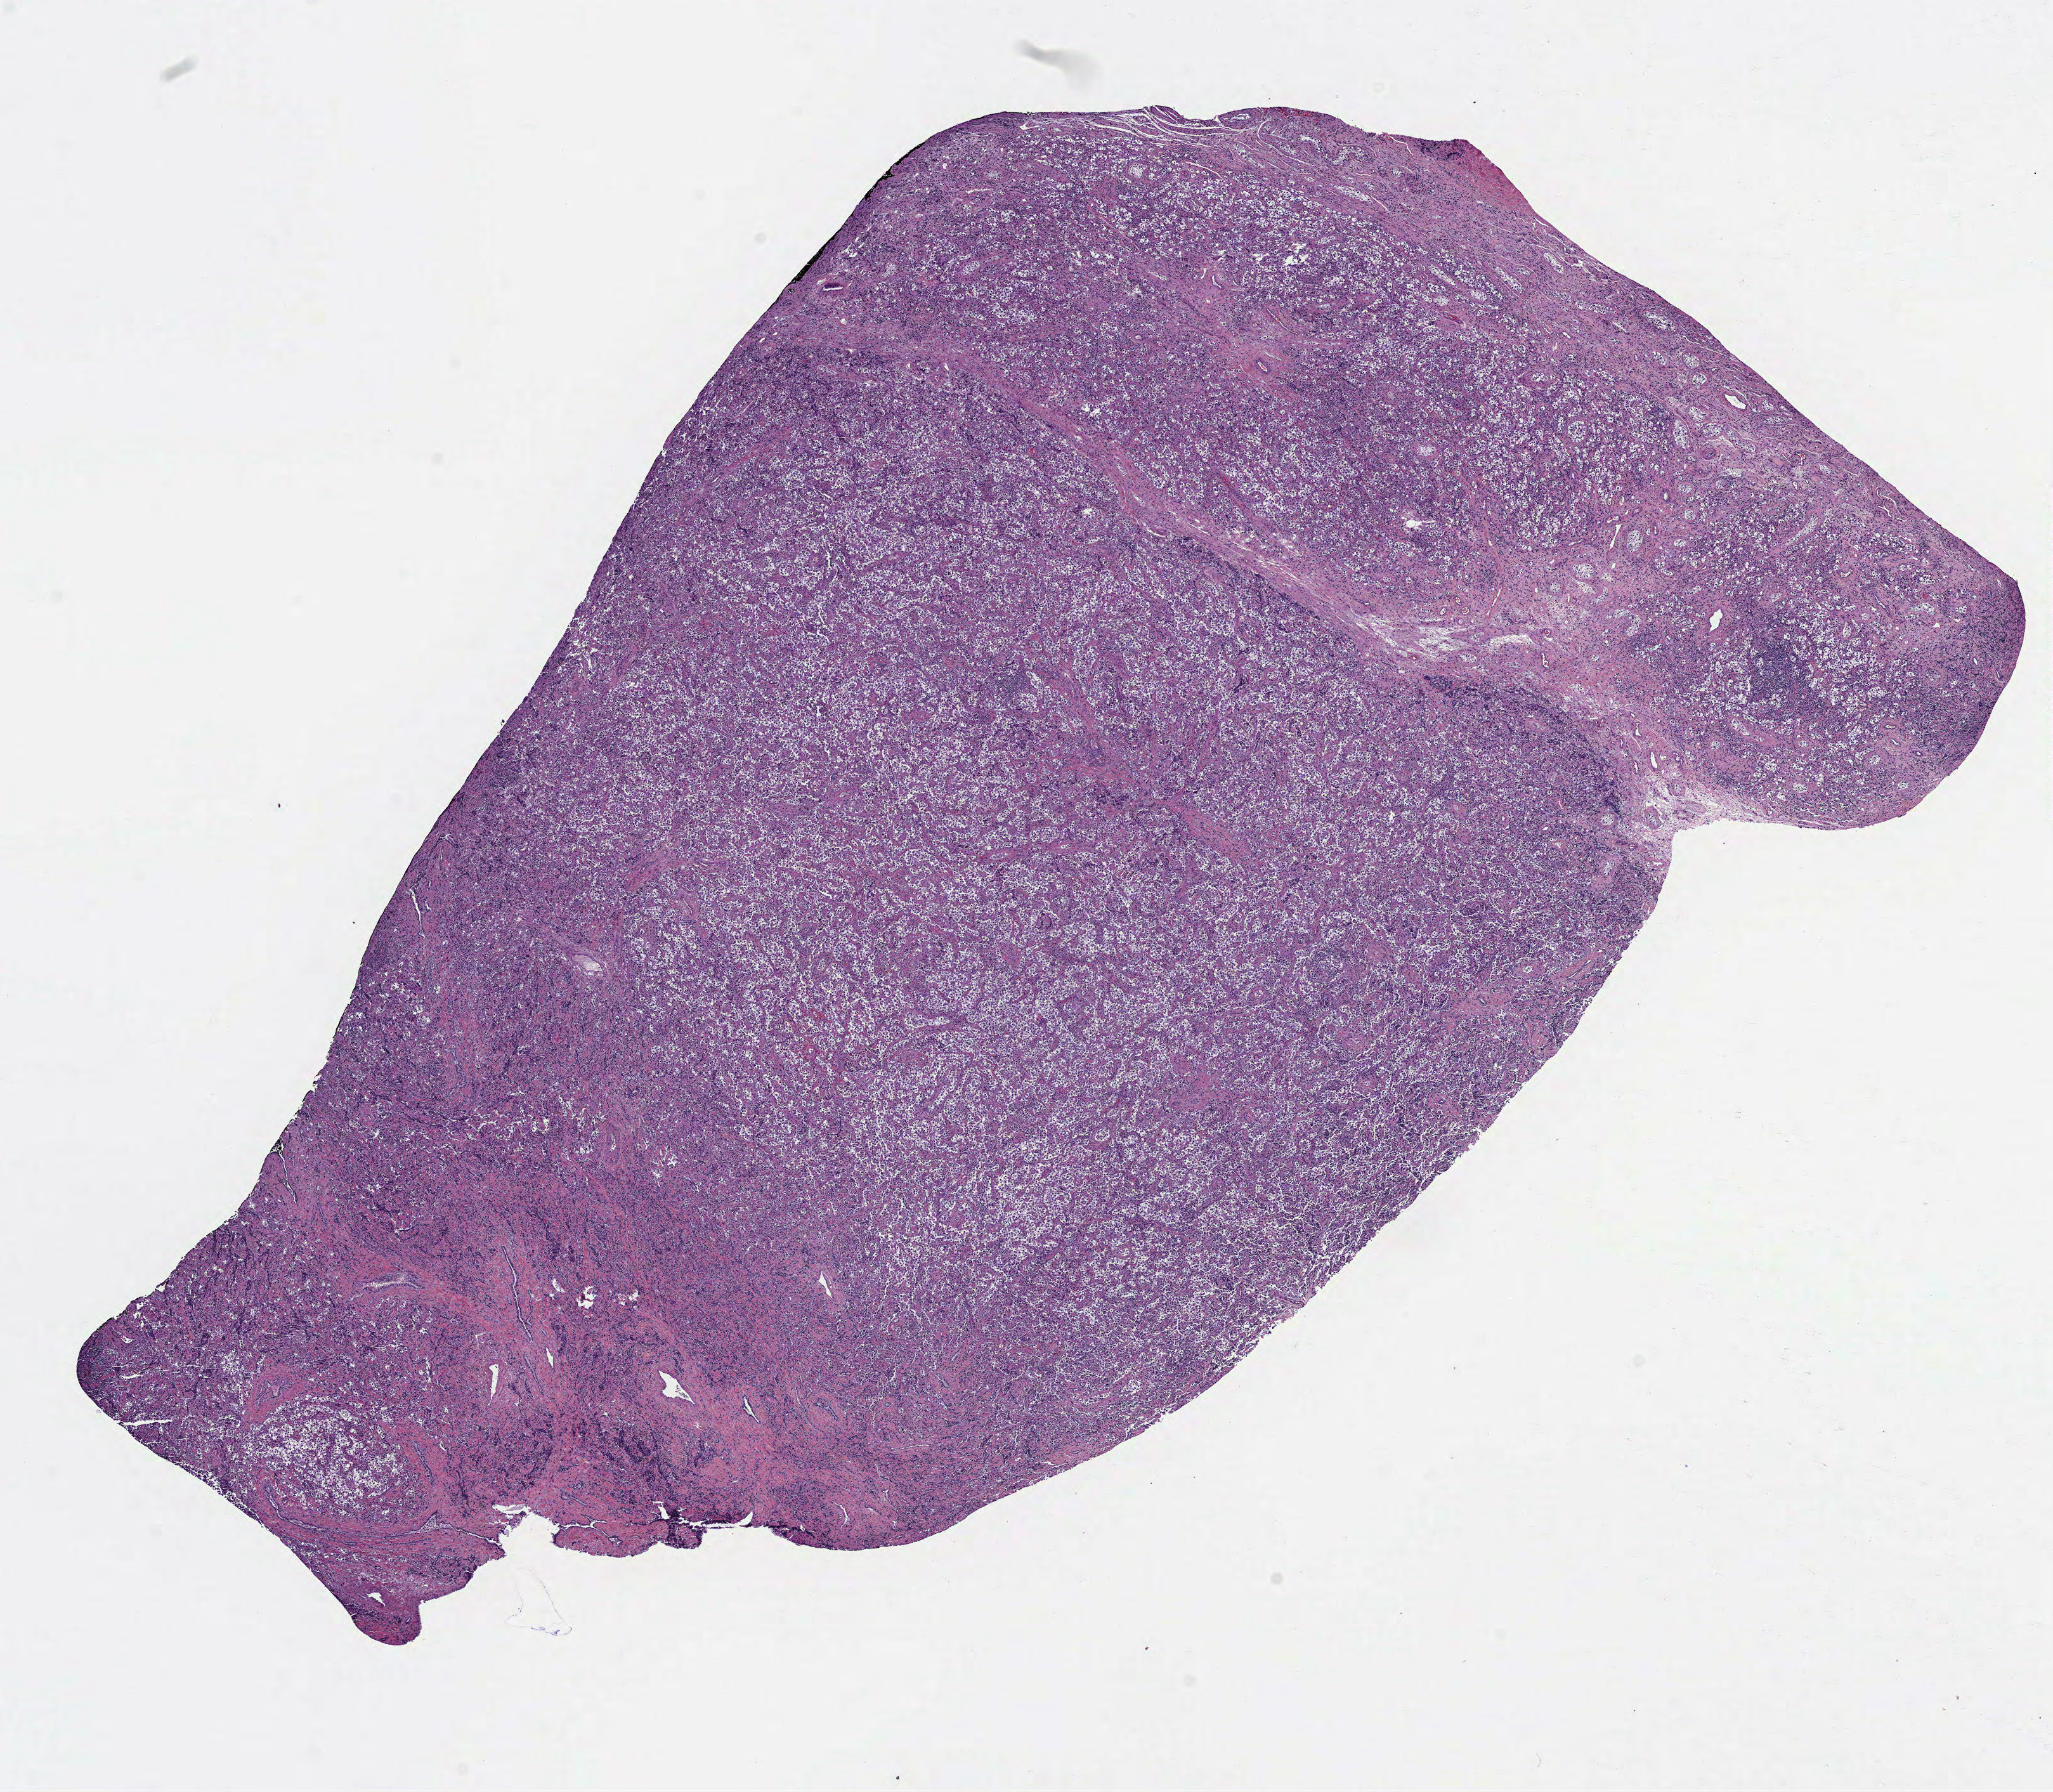
H&E-stained whole-slide image, shown as a low-resolution overview of the whole scanned area (about 13.1 x 11.4 mm, slide scanned at 40x); formalin-fixed paraffin-embedded (FFPE) diagnostic section; primary tumour sample from the testis. Male patient; age at initial diagnosis 28 years.
- AJCC pathologic stage: I
- diagnosis: Seminoma, NOS